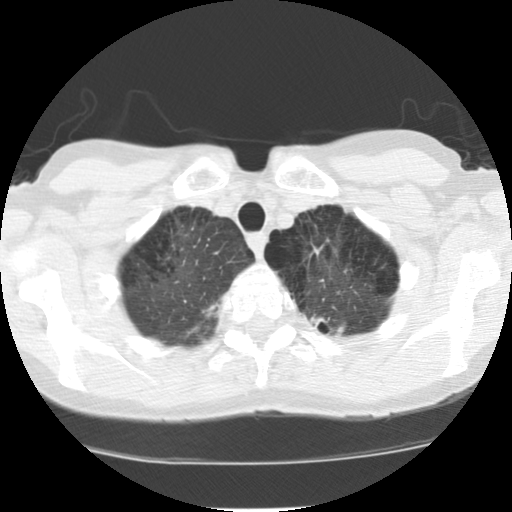
Low-dose screening chest CT, one axial slice; position 102 of 116 along the scan axis; reconstruction kernel STANDARD; 120 kVp; lung window (W 1500 / L -600 HU); 2.5 mm slice thickness; 512 × 512 image matrix.
Annotated regions visible in this slice (manually delineated by an expert):
- lesion 1 (tumor, upper lobe of left lung): bounding box <310,316,344,336> (left, top, right, bottom; pixels)